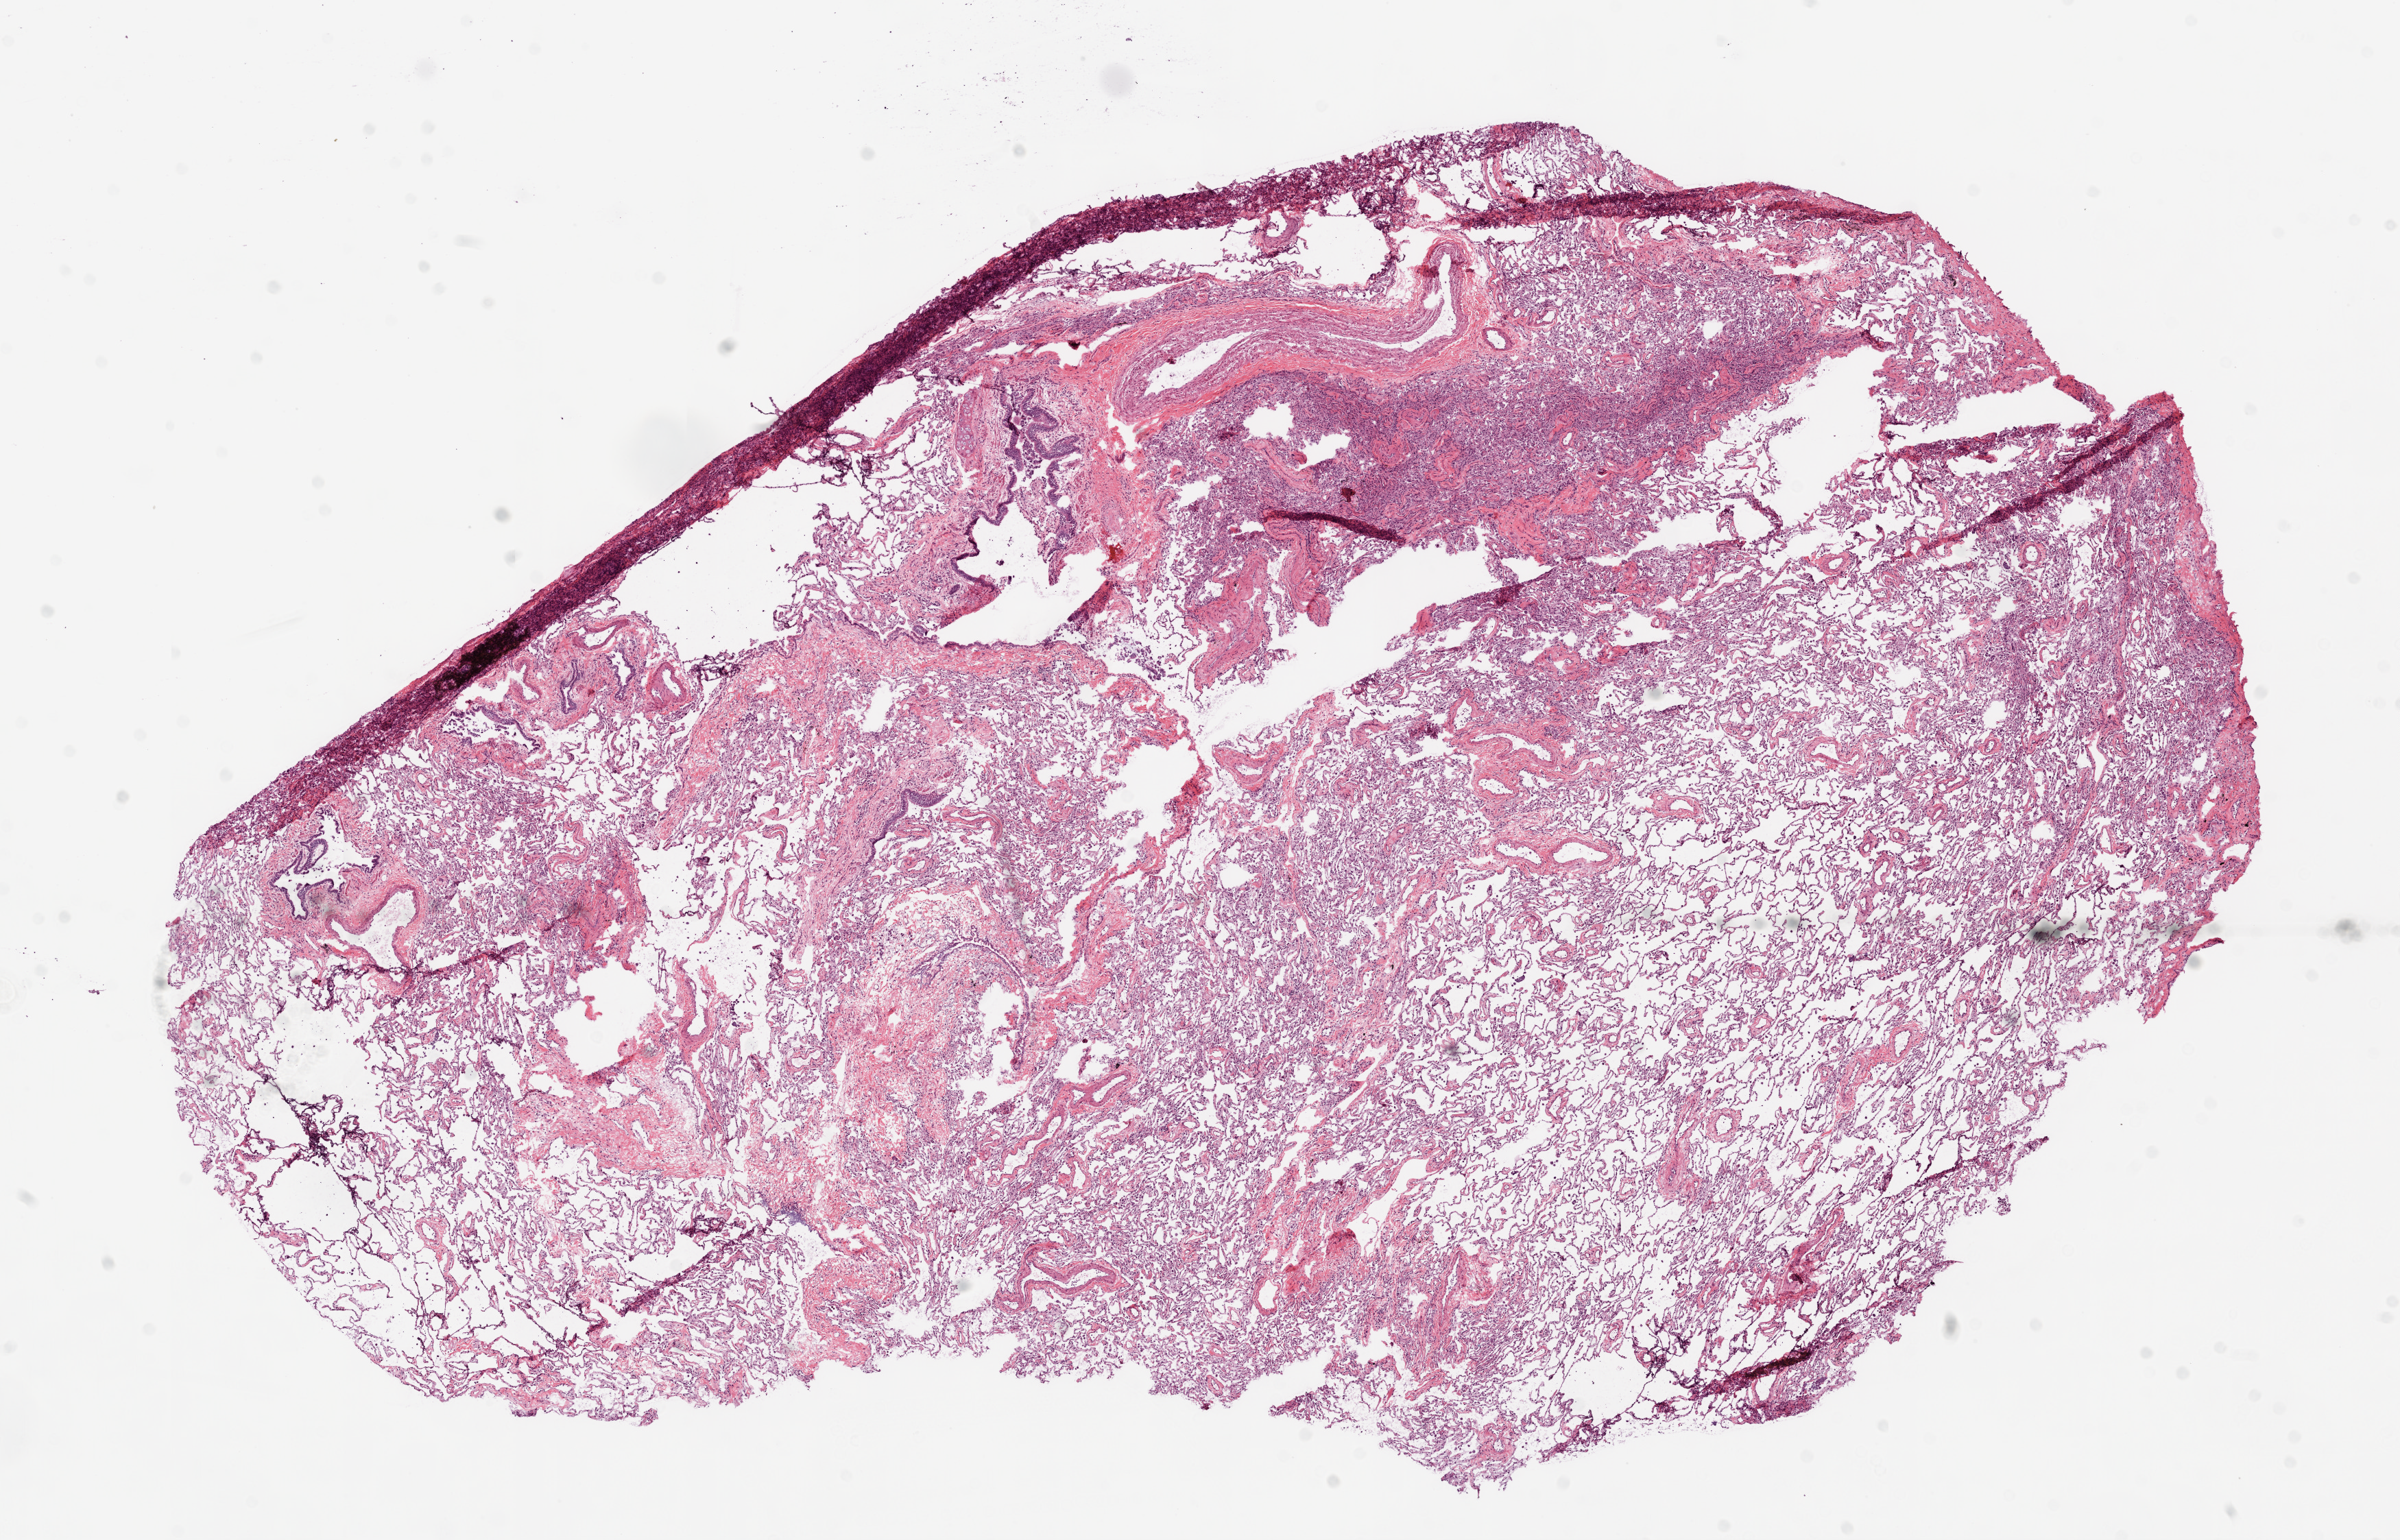
Whole-slide histology image, H&E-stained, a low-resolution overview of the entire scanned area, about 14.0 x 9.0 mm (from a 20x scan); frozen section; solid tissue normal (non-tumour tissue) sample from the lung. Female, age 65 years at initial diagnosis.
This section: solid tissue normal sample (biorepository sample class). Patient diagnosis: Adenocarcinoma, NOS (upper lobe, lung).